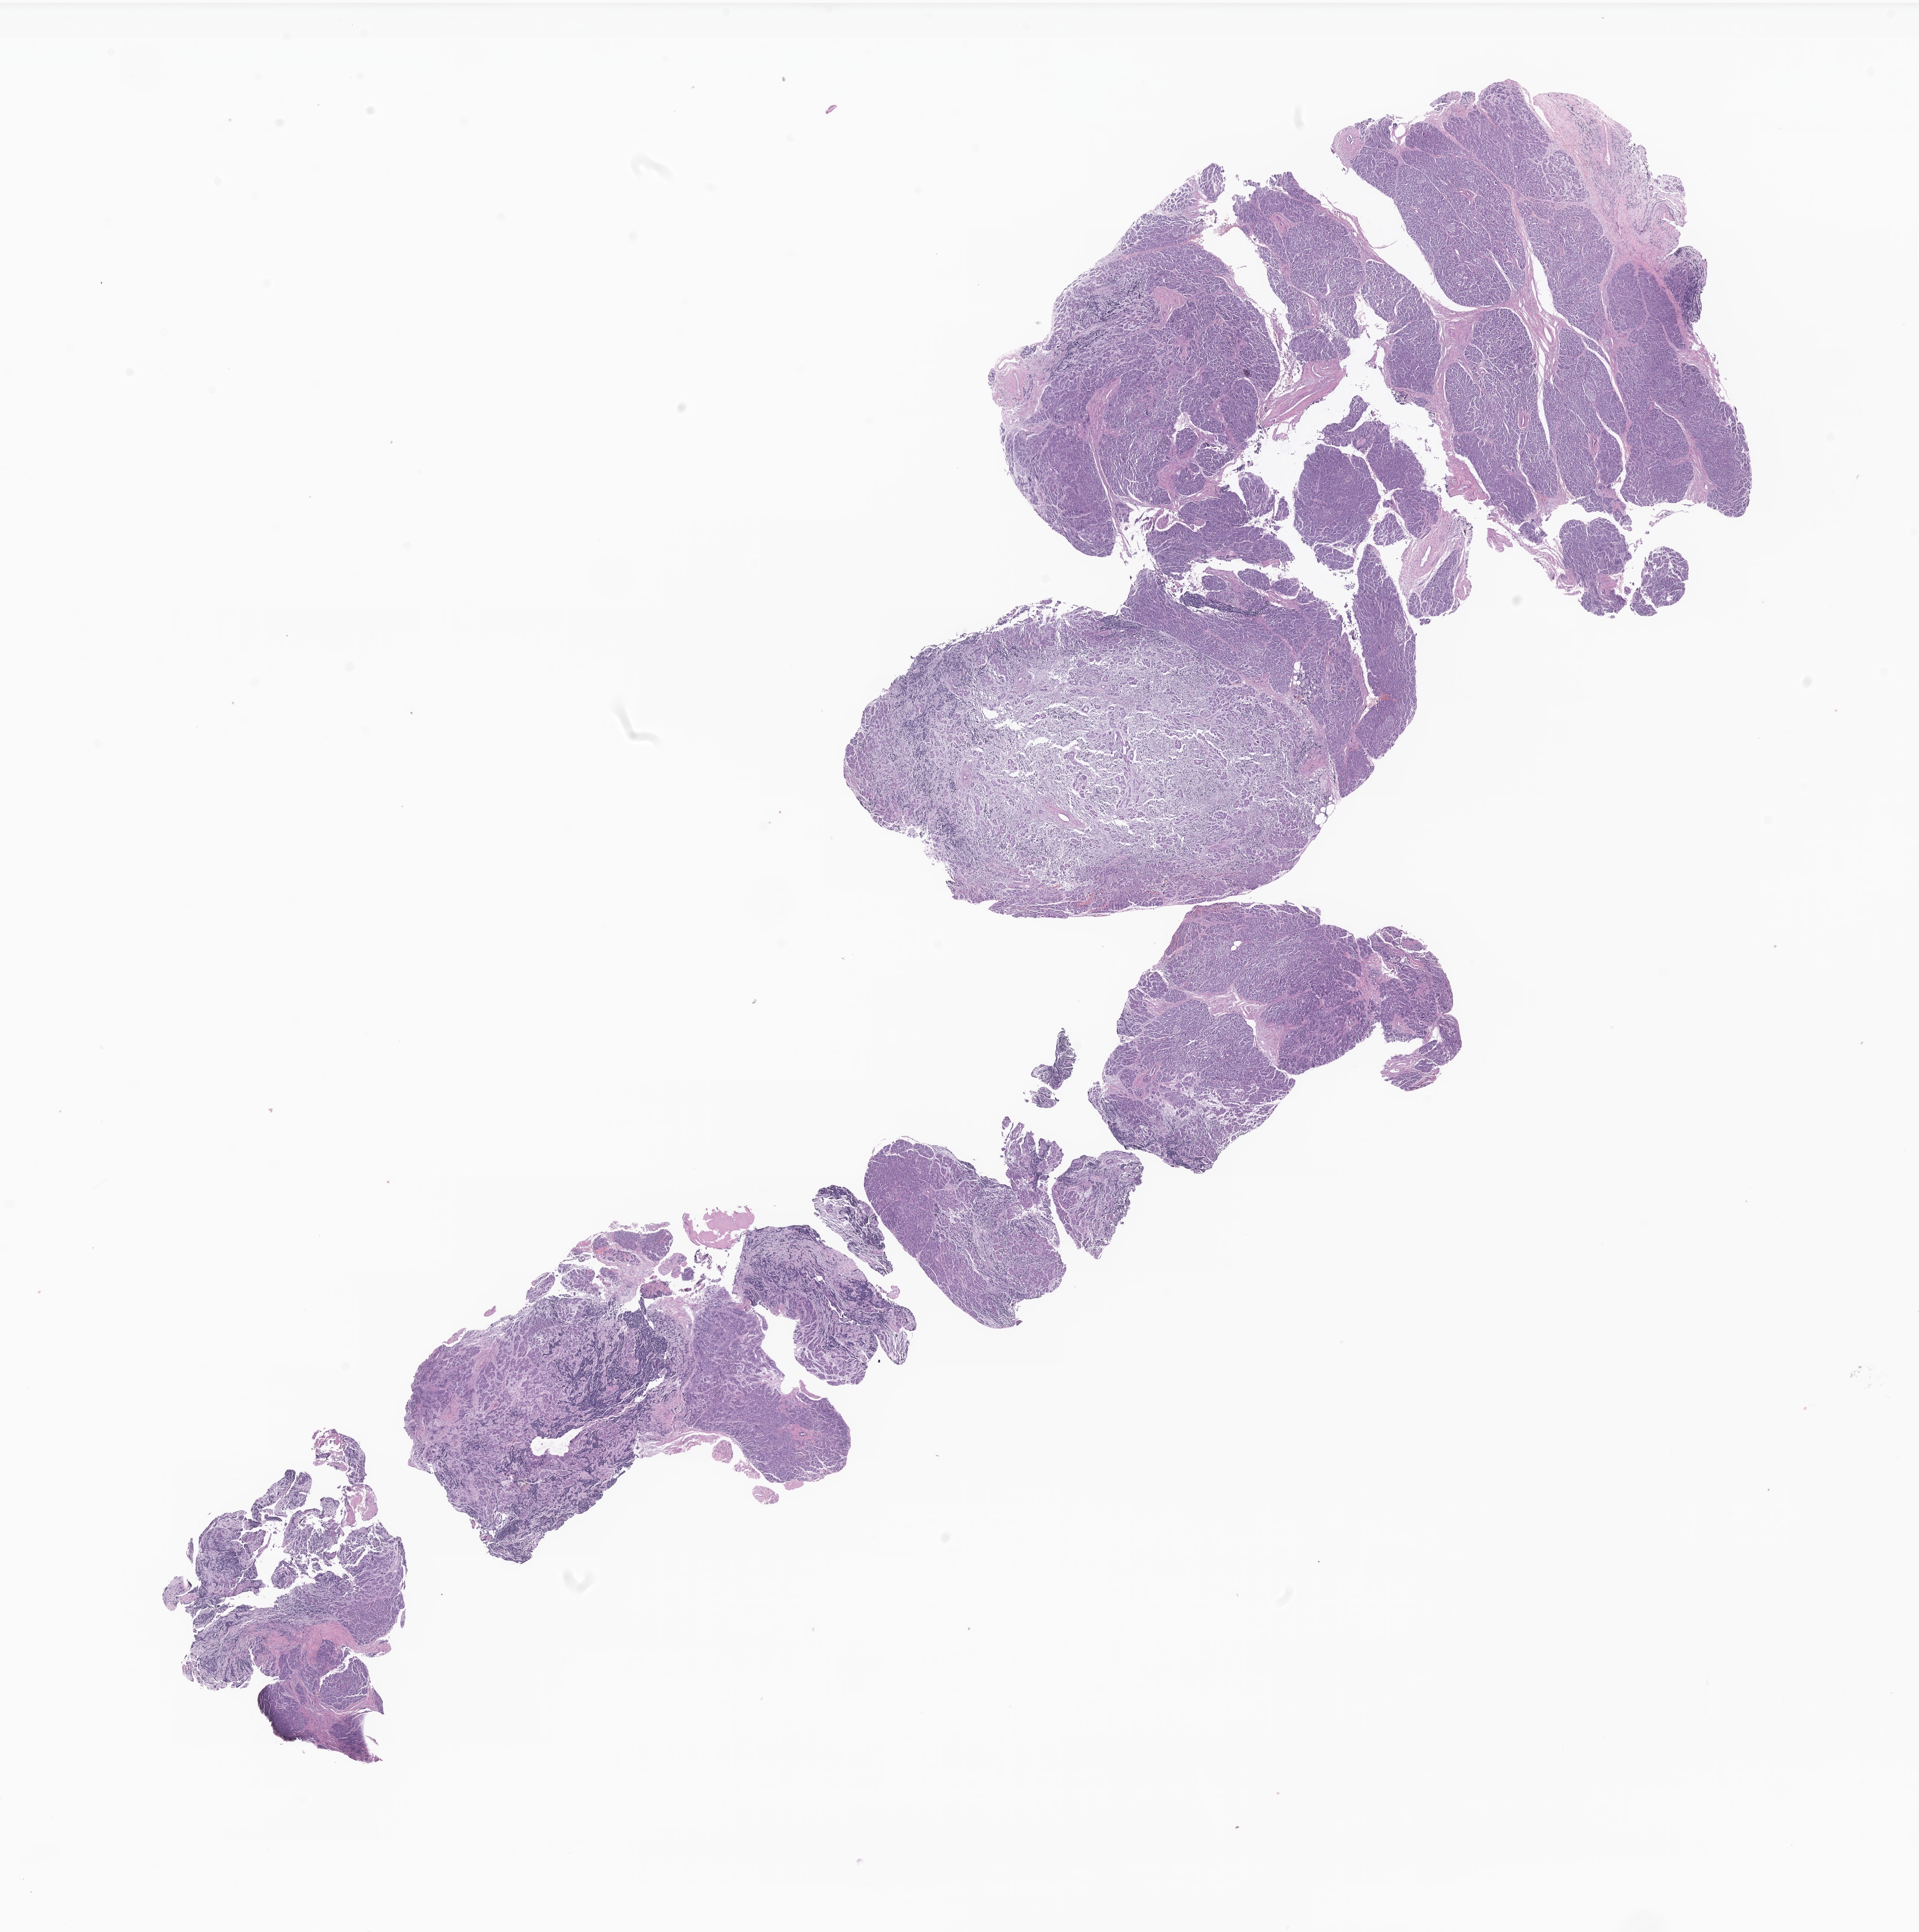
Whole-slide image, haematoxylin and eosin stain of tumor tissue from the retroperitoneum, whole scanned area (about 21.6 x 21.8 mm) shown as a low-resolution overview, formalin-fixed paraffin-embedded section. Patient: male, age 339 days.
Diagnosis: Neuroblastoma, NOS.